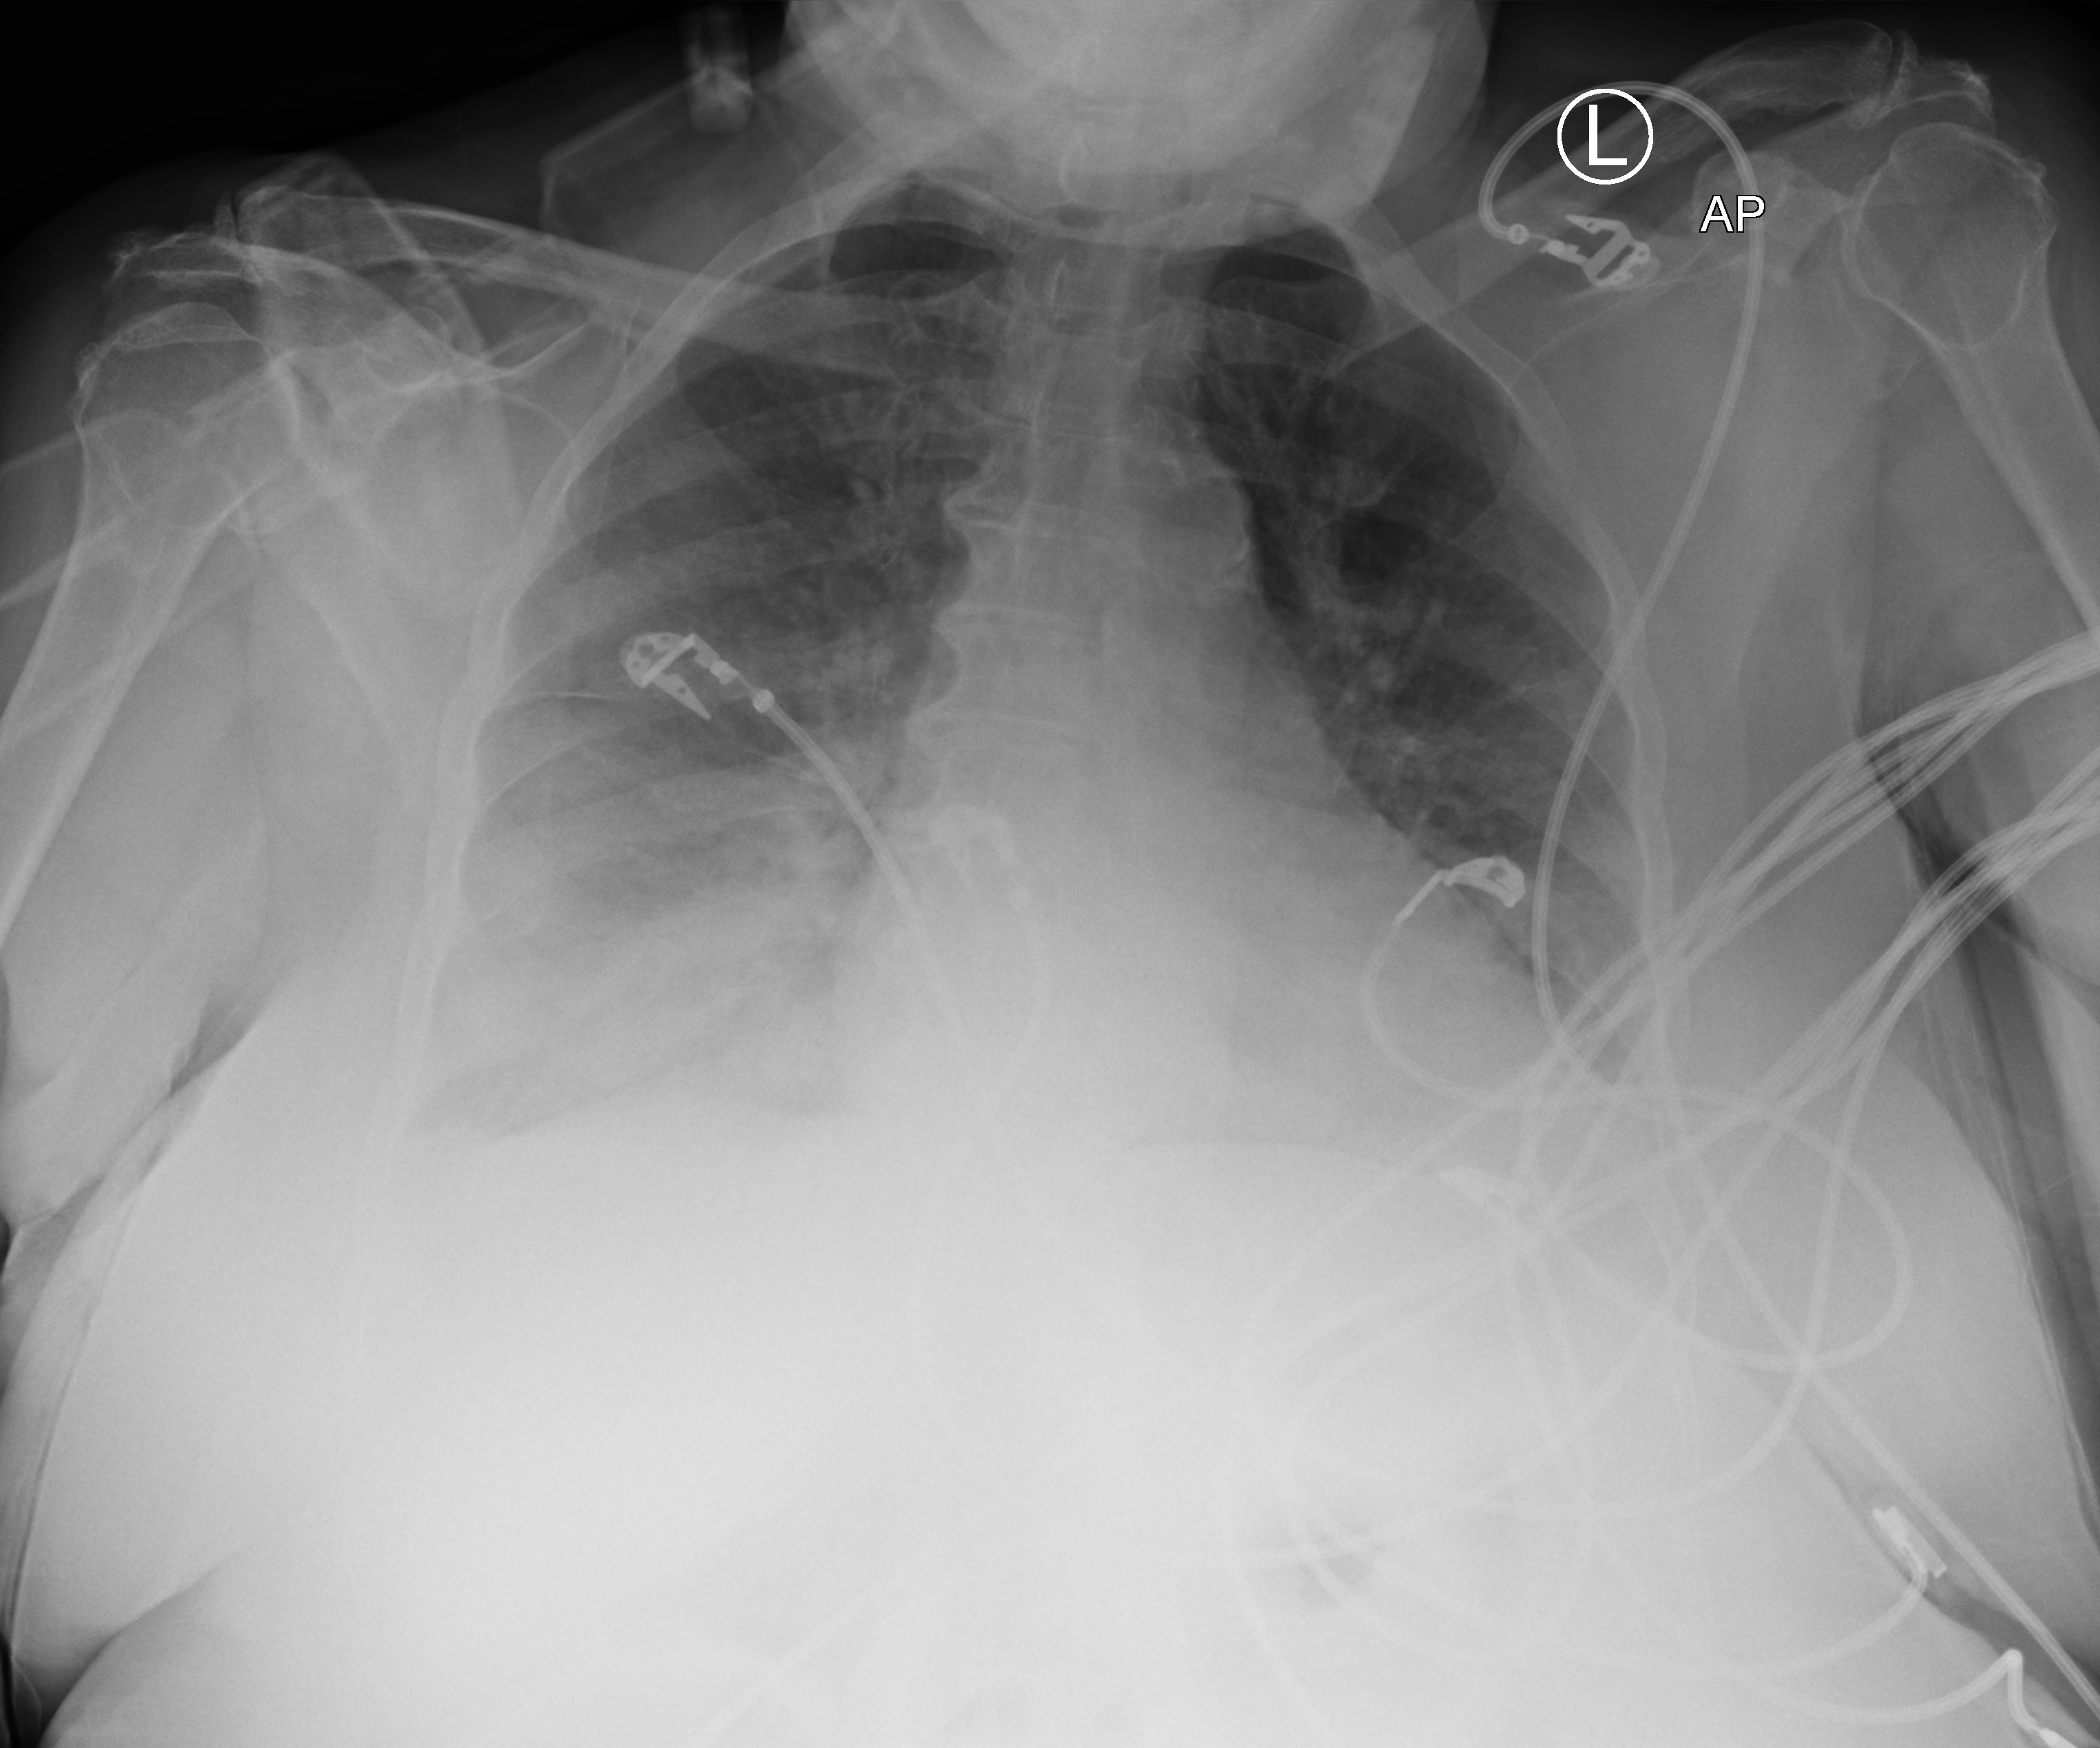
Portable chest radiograph, anteroposterior (AP) projection. Patient hospitalised with COVID-19; female, aged 75–90 years.
Admission-level facts for this patient (not findings on this image; timing relative to this image not recorded): admitted to intensive care during this hospital stay: no; mechanically ventilated during this hospital stay: no; hypertension (admission record): yes.